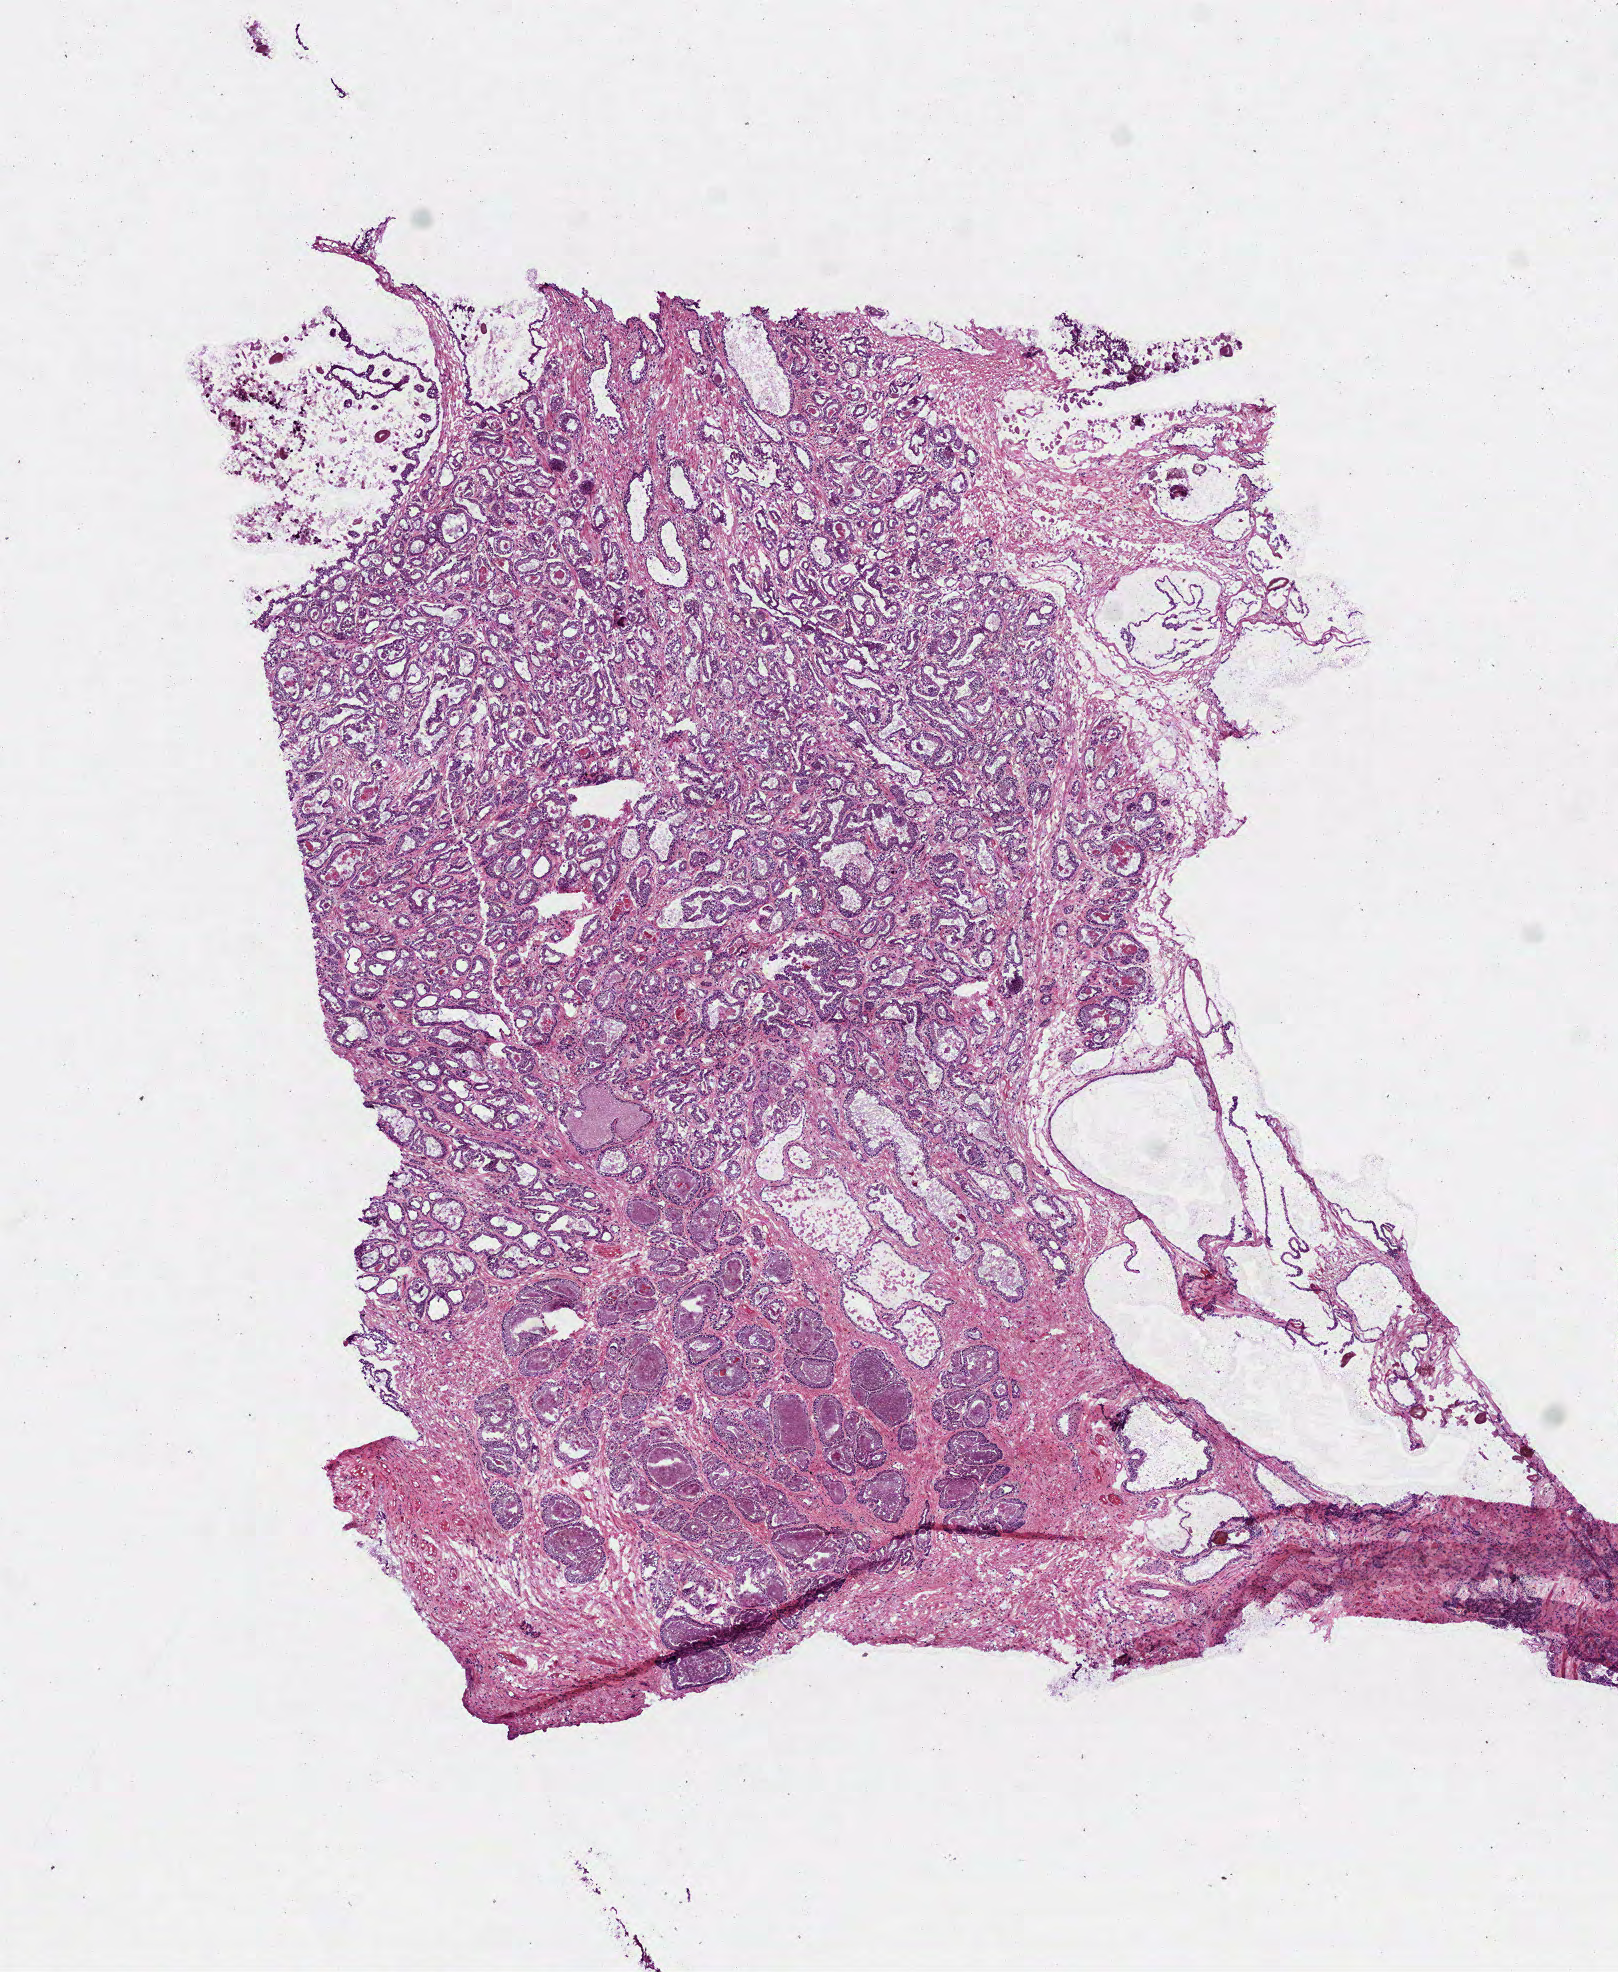
Whole-slide histology image, H&E-stained, whole scanned area (about 6.5 x 8.0 mm, from a 40x scan) shown as a low-resolution overview. Frozen section. Primary tumour sample from the prostate. Patient: male, age at initial diagnosis 62 years. Gleason score: 7 (4+3). Pathologist review of this section (percent, as recorded): tumour cells 70%, tumour nuclei 75%, normal cells 15%, stromal cells 10%, necrosis 5%. Inflammatory infiltration, as recorded: lymphocyte infiltration 1%, monocyte infiltration 0%, neutrophil infiltration 0%.
* laterality: bilateral
* histologic diagnosis: Acinar cell carcinoma (prostate gland)